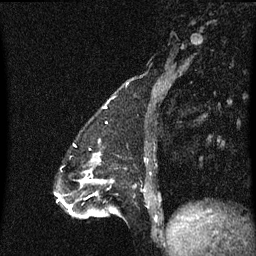
Breast MRI (dynamic contrast-enhanced), one sagittal slice; dynamic contrast-enhanced series, image 2 of 3 at this slice position (ordered by acquisition); 1.5 T; TE 4.2 ms, TR 8.4 ms; 256 × 256 image matrix, field of view 200 × 200 mm. Patient: female, 47 years.
Annotated regions visible in this slice (semi-automatic segmentation, software-assisted and operator-edited):
- analysis volume of interest (the breast-tissue region the enhancement analysis was run in; not a lesion): bounding box (x1, y1, x2, y2) in pixels: (100, 180, 150, 217)
- tumour enhancement mask (voxels above the 70 % enhancement threshold inside the analysis volume of interest): (100, 180, 106, 183)